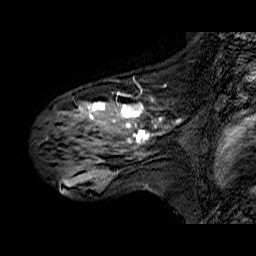
Breast MRI (dynamic contrast-enhanced), one sagittal slice; slice 40 of 60 in the series (ordered by position); dynamic contrast-enhanced series, time point 2 of 6 at this slice position (early post-contrast); 1.5 T; TE 6.3 ms, TR 32.9 ms; 4 mm slice thickness; 256 × 256 image matrix, field of view 200 × 200 mm. Female patient. Case-level facts recorded for this patient, not image findings: setting: breast cancer imaged before/during neoadjuvant chemotherapy; receptor status: HER2-positive.
Annotated regions visible in this slice (semi-automatically segmented with operator editing):
- analysis volume of interest (the breast-tissue region the enhancement analysis was run in; not a lesion): bounding box (x1, y1, x2, y2) in pixels: (45, 85, 174, 173)
- tumour enhancement mask (voxels above the 100 % enhancement threshold inside the analysis volume of interest): (88, 103, 162, 144)